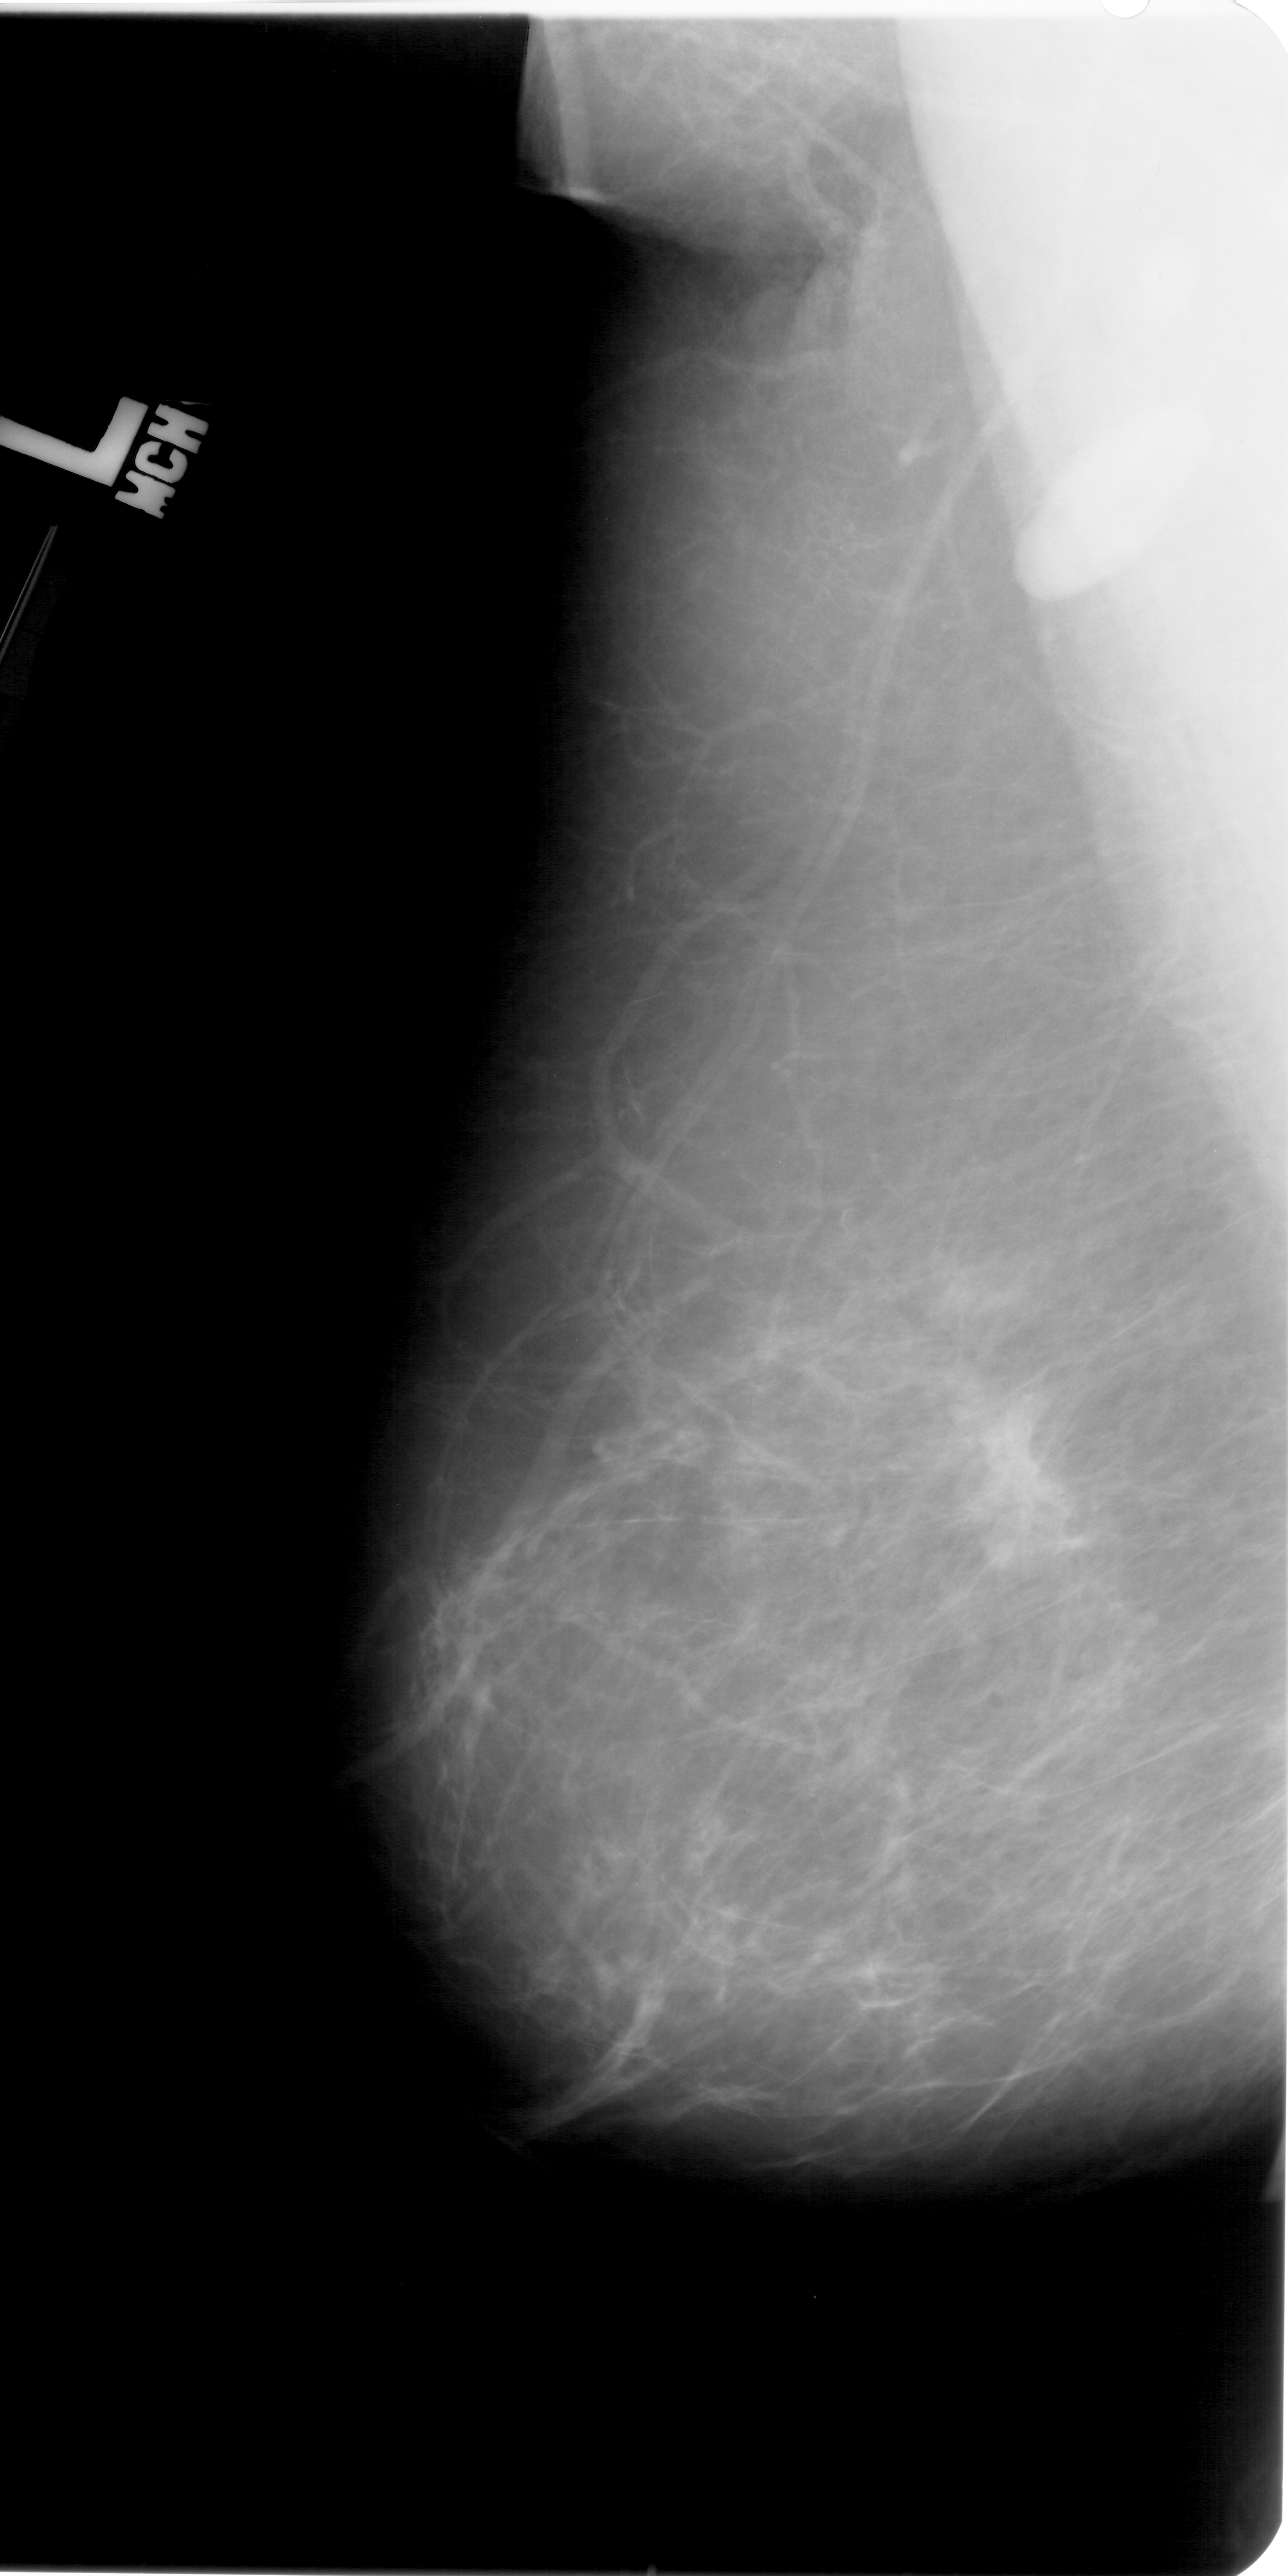
Mammogram (digitized film), left breast, mediolateral oblique (MLO) view, breast composition: scattered fibroglandular densities (BI-RADS density category 2 of 4).
Marked findings (only marked abnormalities are described; nothing is implied about the rest of the image): mass, shape irregular, margins spiculated; BI-RADS assessment category 5; pathology (as recorded): malignant.